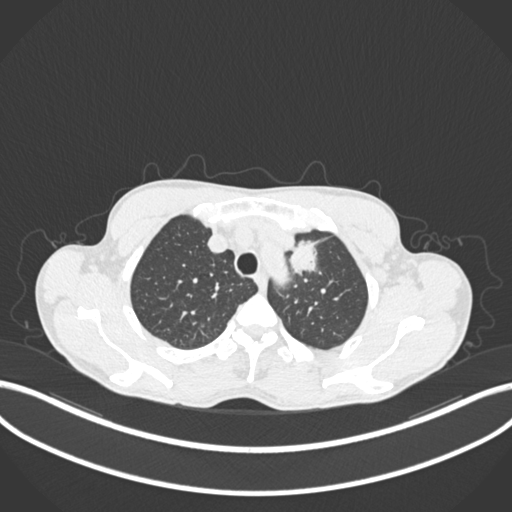
Chest CT, one axial slice; slice 168 of 211 in the series (ordered by position); reconstruction kernel B30f; lung window (W 1500 / L -600 HU); 512 × 512 image matrix. Patient: male, 58 years. From the clinical record (not read from this slice): clinical TNM (as recorded): T1c N1 M0.
Annotated regions visible in this slice (rectangle marked by the reading radiologist):
- lung tumour (recorded histology: adenocarcinoma): box from (x=280, y=233) to (x=319, y=285) px